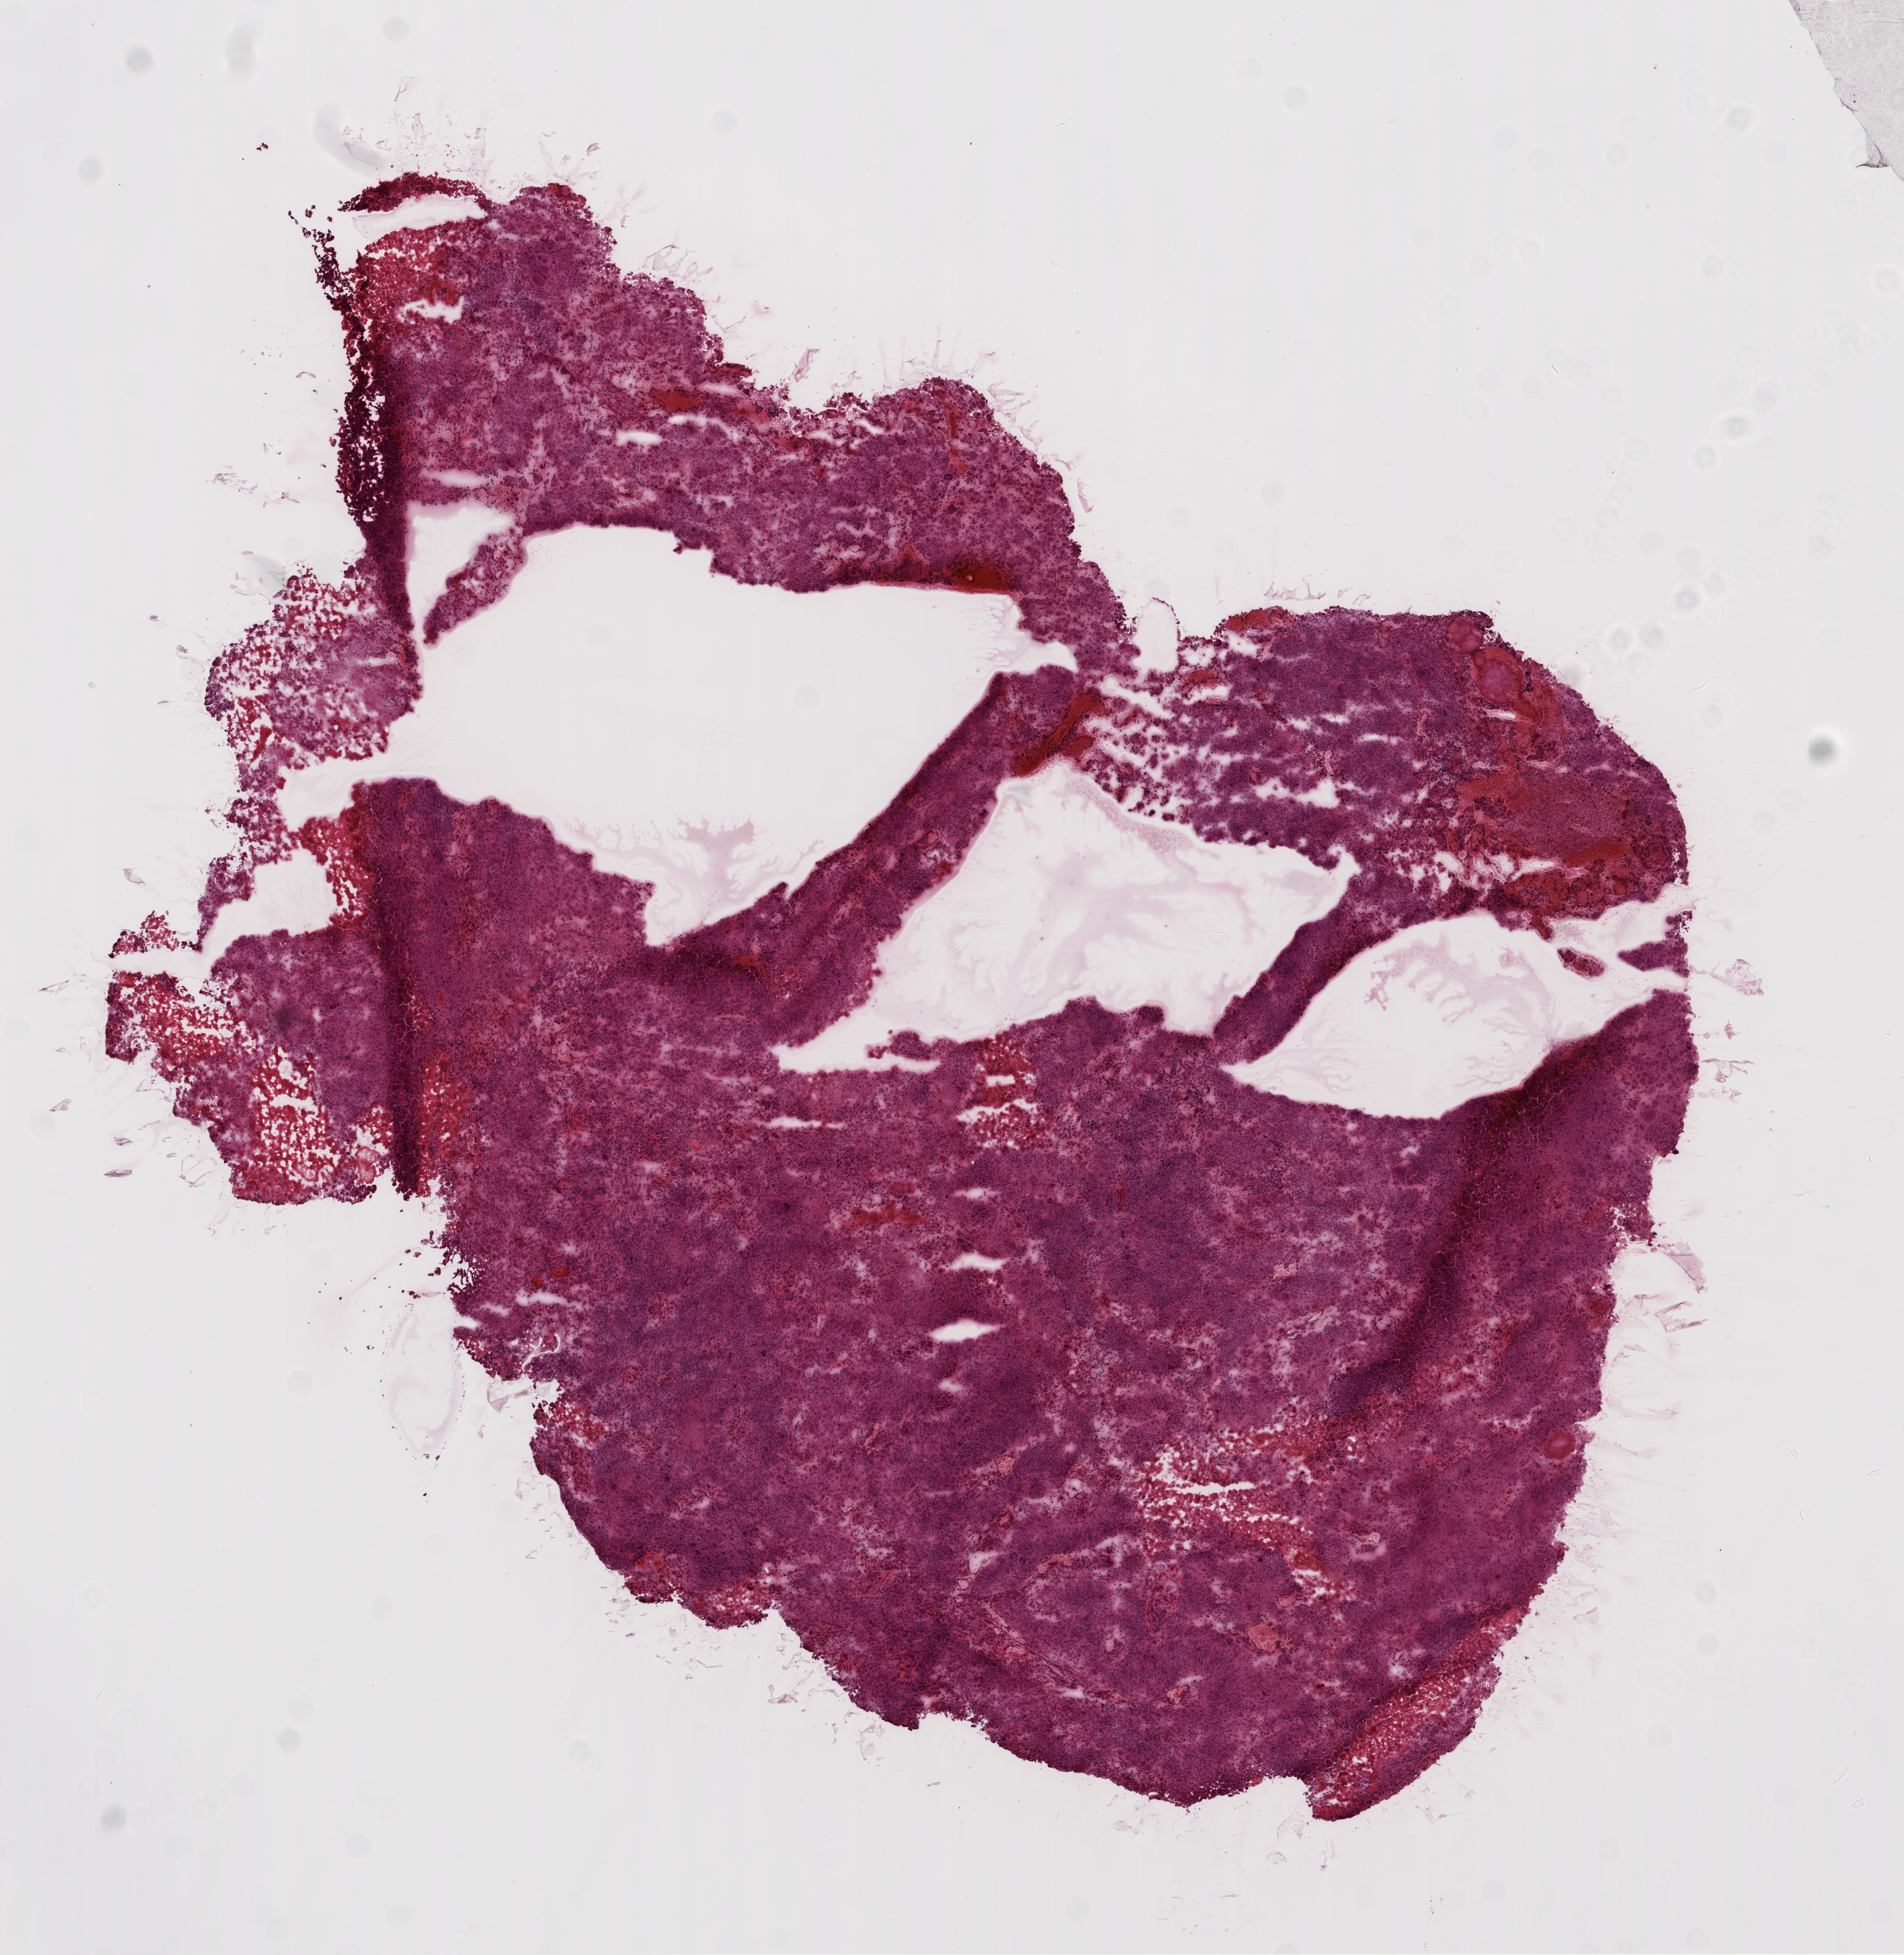
Hematoxylin and eosin (H&E) stained whole-slide image — a low-resolution overview of the entire scanned area, about 9.7 x 9.9 mm (from a 20x scan). Frozen section. Brain, primary tumour sample. Patient: male, age at initial diagnosis 24 years. Composition of this section per pathologist review: tumour cells 80%, tumour nuclei 100%, normal cells 0%, stromal cells 0%, necrosis 20%.
* diagnosis: Glioblastoma